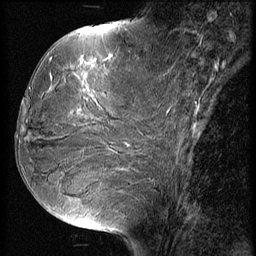
Breast MRI (dynamic contrast-enhanced), one sagittal slice; position 24 of 56 along the scan axis; 3 images stored at this slice position (order not interpretable as contrast timing); 1.5 T; TE 4.2 ms, TR 9 ms; 2.5 mm slice thickness; 256 × 256 image matrix, field of view 180 × 180 mm. Female patient, age 51 years. Case-level facts recorded for this patient, not image findings: setting: breast cancer imaged before/during neoadjuvant chemotherapy; receptor status: HR-positive, HER2-negative.
Structures marked on this image (semi-automatic segmentation, software-assisted and operator-edited):
- analysis volume of interest (the breast-tissue region the enhancement analysis was run in; not a lesion): bounding box <23,56,156,165> (left, top, right, bottom; pixels)
- tumour enhancement mask (voxels above the 140 % enhancement threshold inside the analysis volume of interest): <77,56,110,117>